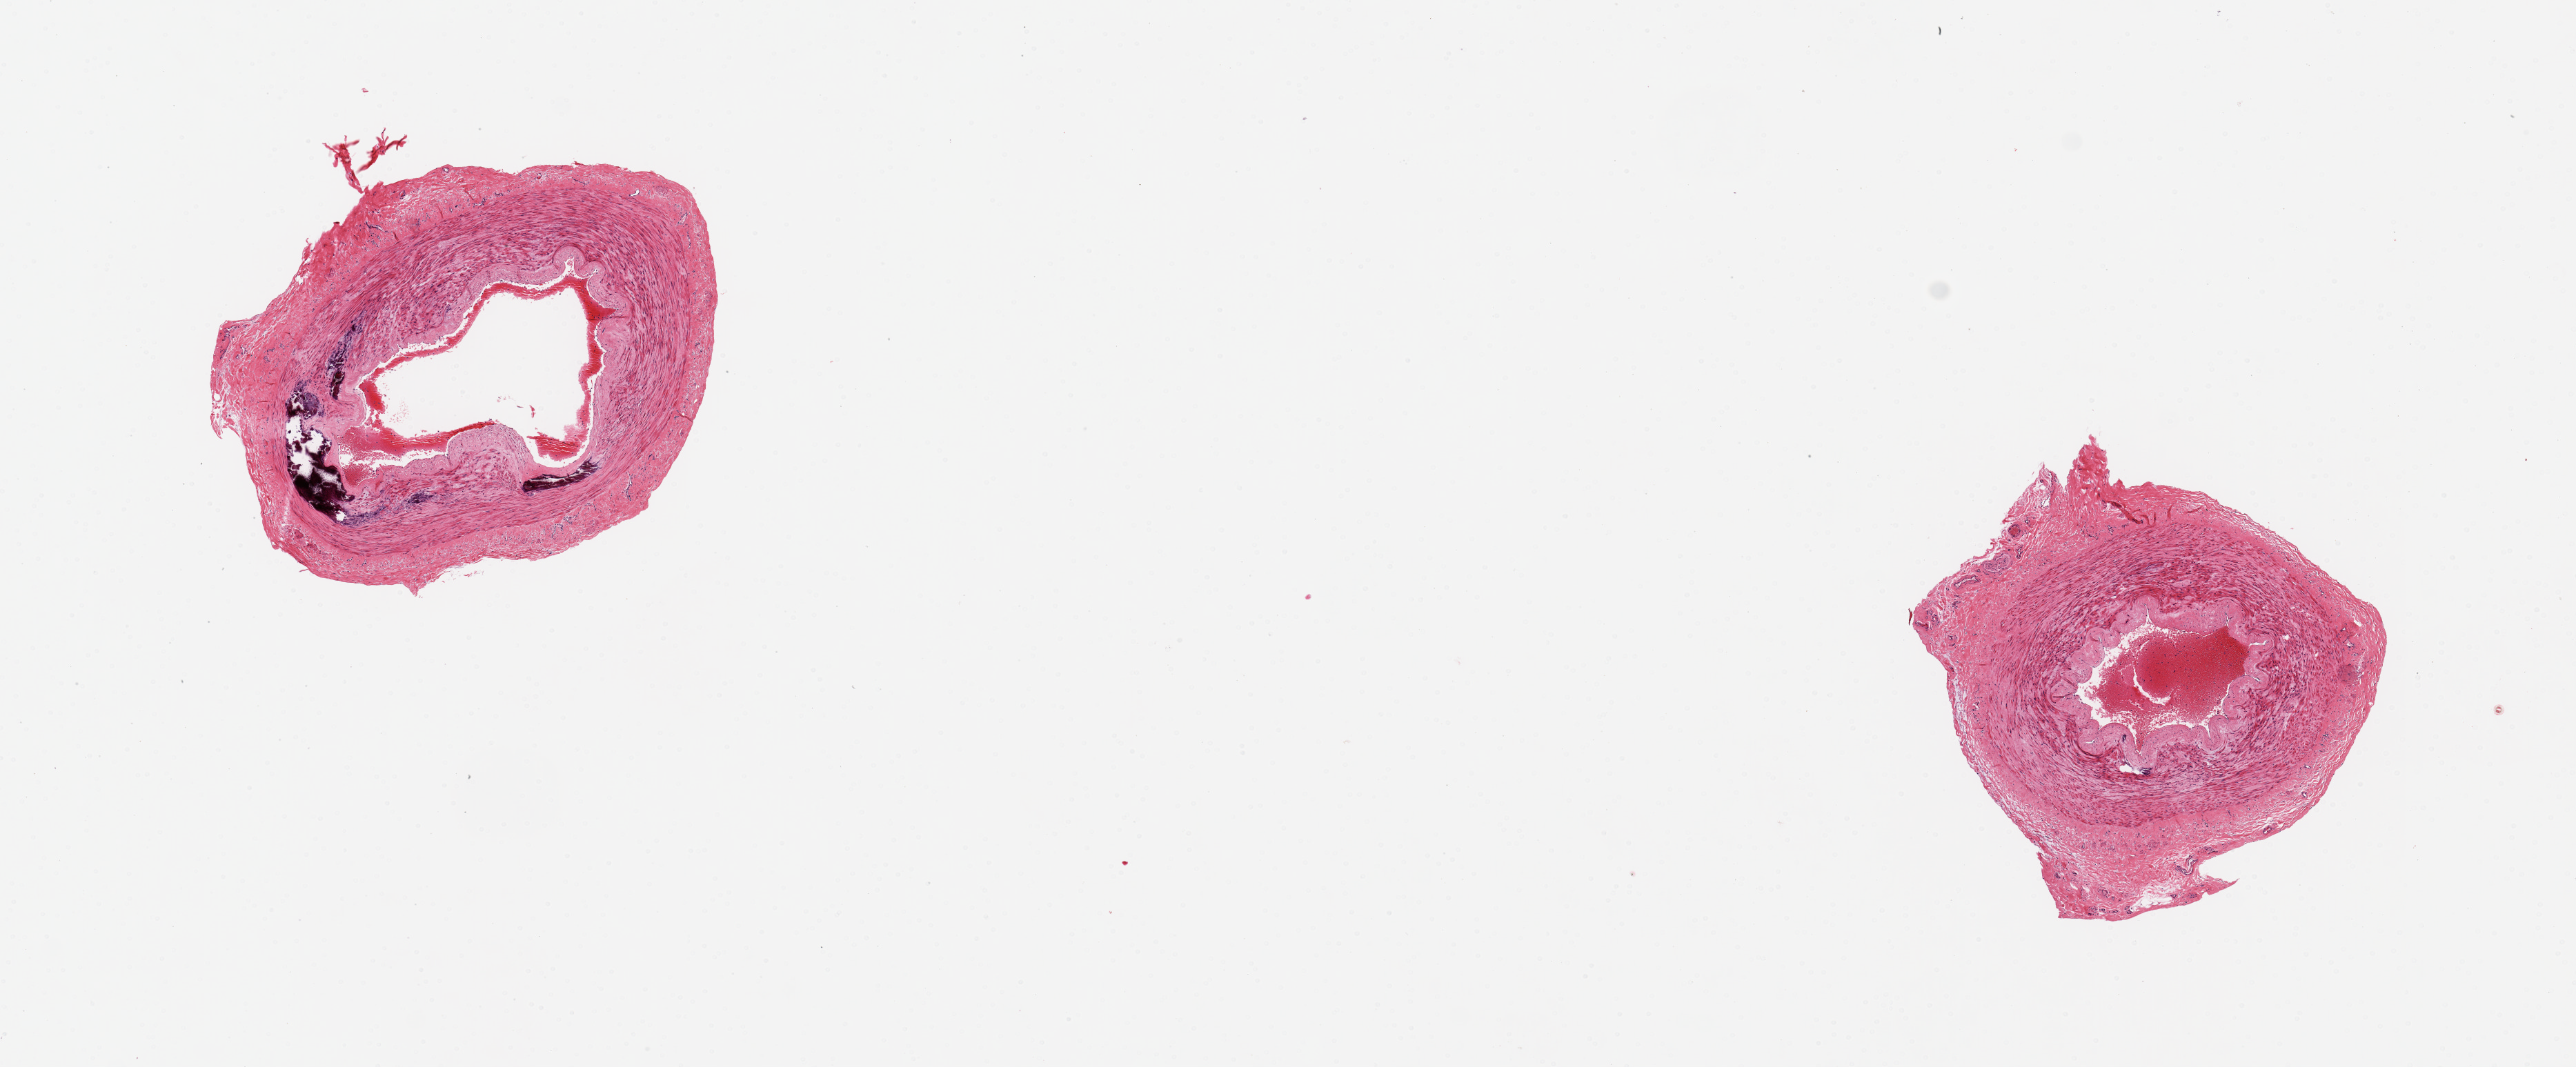
Hematoxylin and eosin (H&E) whole-slide image, low-resolution overview of the scanned area, about 14.8 x 6.1 mm, PAXgene-fixed paraffin-embedded (PFPE) section, target tissue: tibial artery, donor tissue sample. Donor sex: male.
Review note (as recorded): 2 pieces ~2.5mm d; Good clean specimens.